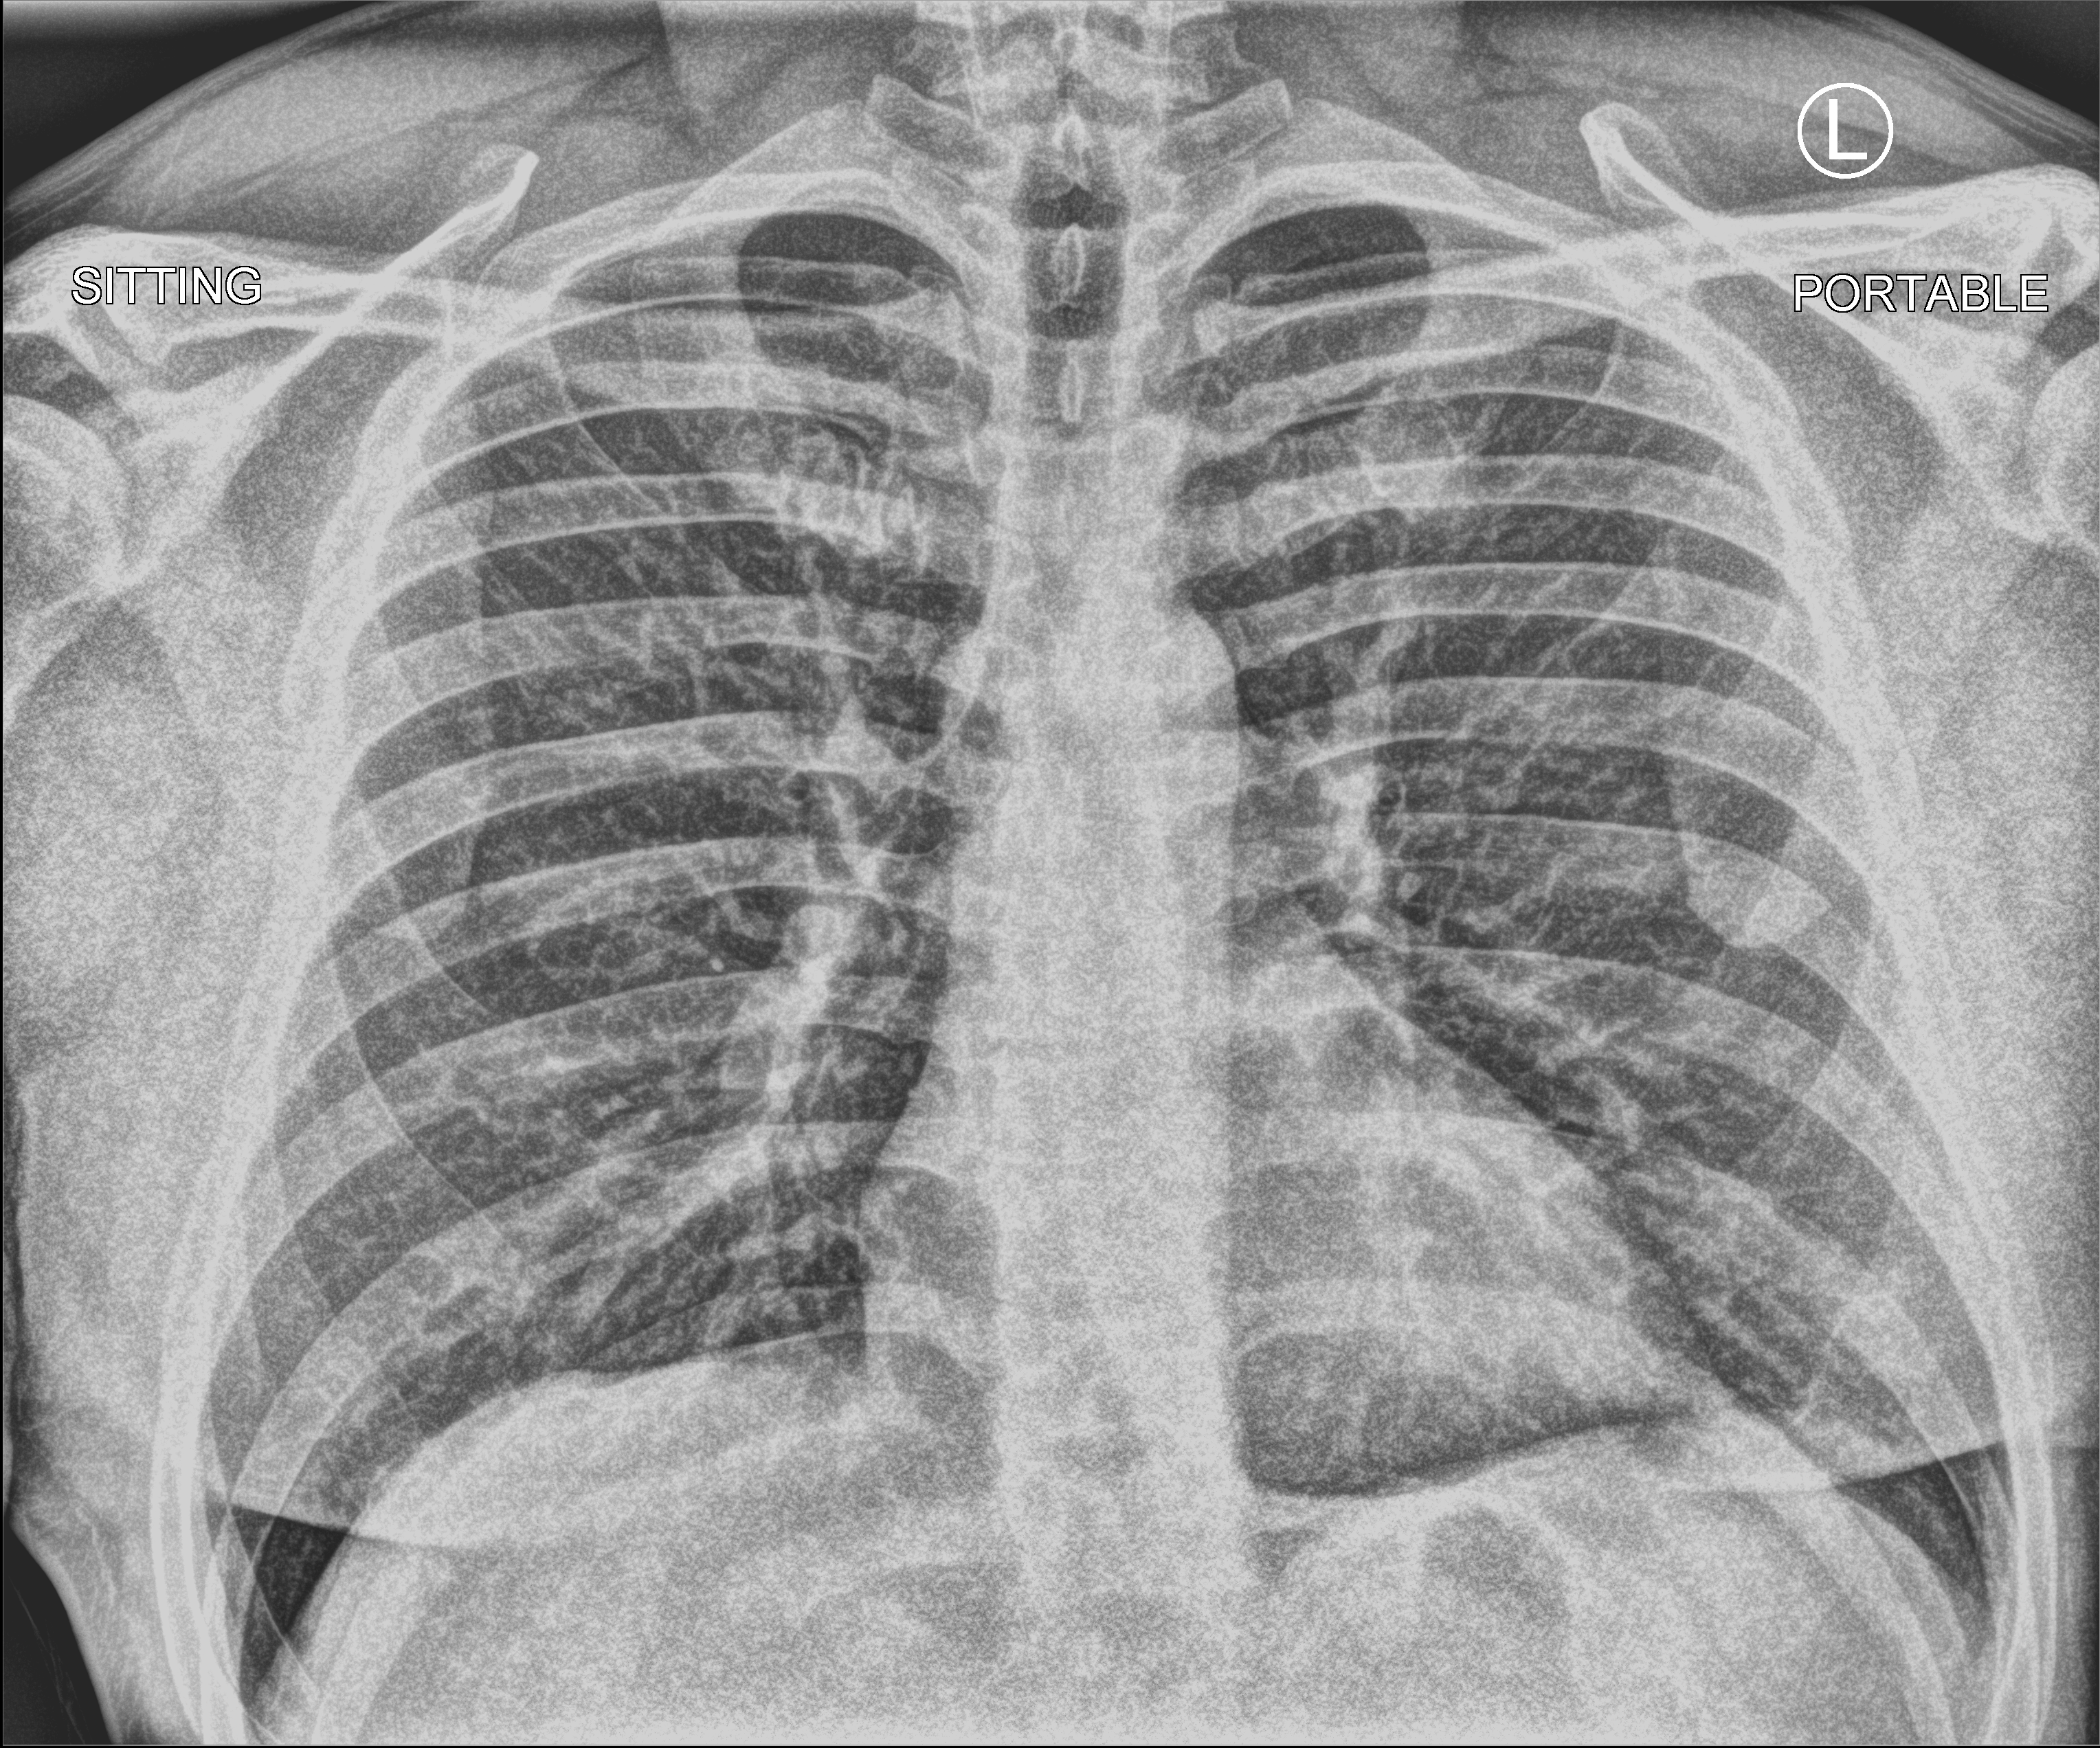
Bedside chest radiograph (computed radiography); anteroposterior (AP) projection. Male patient hospitalised with COVID-19, age 18–59 years.
From the hospital-stay record, not from the radiograph (when in the stay this image was taken is not recorded): admitted to intensive care during this hospital stay: no.